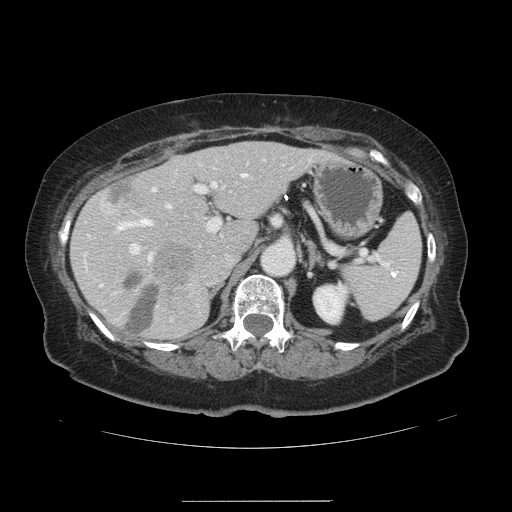
Contrast-enhanced abdominal CT, one axial slice; slice 81 of 141 in the series (ordered by position); 120 kVp; intravenous contrast given; soft-tissue window (W 400 / L 40 HU); 512 × 512 image matrix. Female patient, age 74 years. From the clinical record (not read from this slice): diagnosis: colorectal cancer liver metastases, imaged before liver resection; multiple liver metastases: yes; largest metastasis: 7 cm; chemotherapy before resection: no.
Annotated regions visible in this slice (outlined manually by an expert reader):
- hepatic veins: bounding box <117,173,246,230> (left, top, right, bottom; pixels)
- liver: <72,143,327,342>
- planned liver remnant (the part of the liver to remain after resection): <72,143,327,340>
- portal vein (with intrahepatic branches): <129,159,264,260>
- liver metastasis: <103,176,141,214>
- liver metastasis: <124,273,161,335>
- liver metastasis: <156,243,194,294>